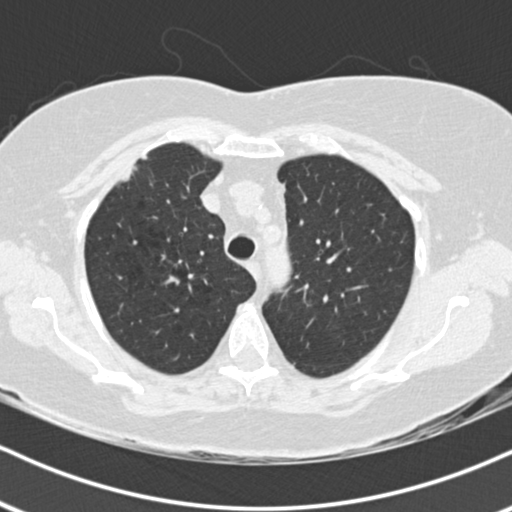
Low-dose screening chest CT, one axial slice; slice 141 of 178 in the series (ordered by position); reconstruction kernel B30f; 120 kVp; lung window (W 1500 / L -600 HU); 2 mm slice thickness; 512 × 512 image matrix, field of view 320 × 320 mm.
Annotated regions visible in this slice (expert manual segmentation):
- lesion 1 (tumor, upper lobe of right lung): box from (x=121, y=153) to (x=148, y=182) px